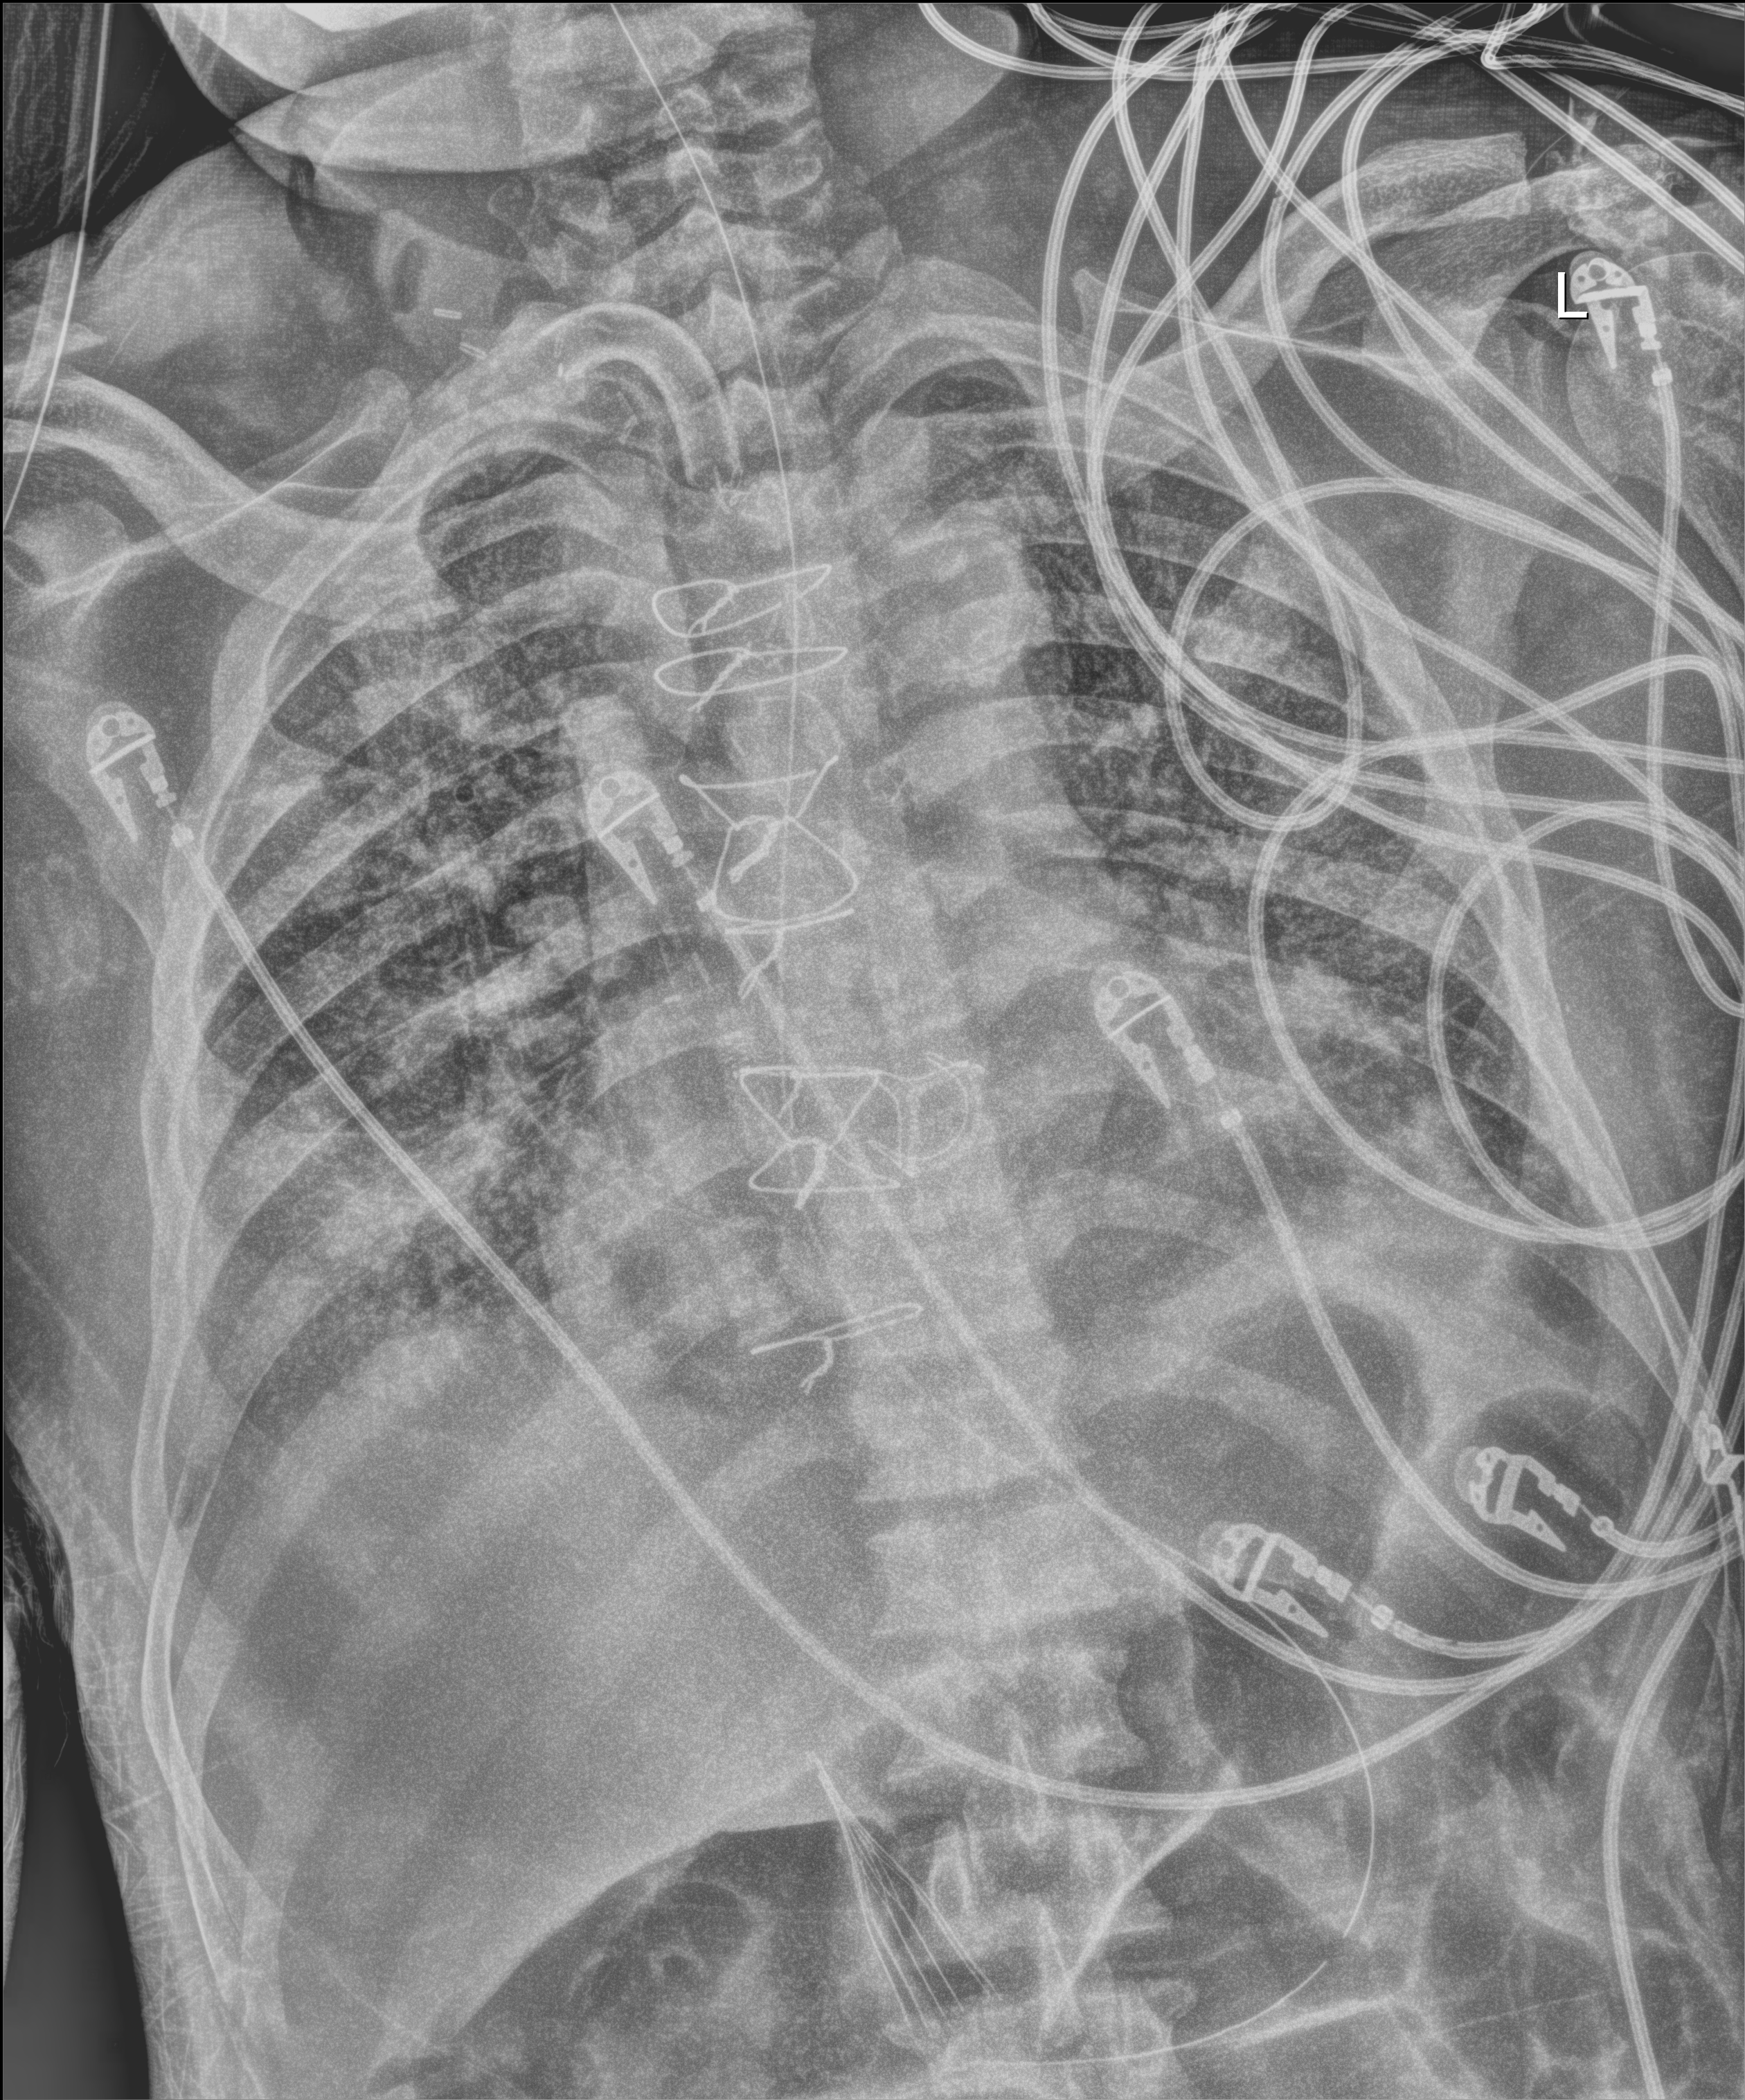
Portable chest radiograph. Patient hospitalised with COVID-19; male, aged 60–74 years.
Hospital-stay facts (about this admission, not read from this image; timing relative to this image not recorded): hypertension (admission record): no; admitted to intensive care during this hospital stay: yes; diabetes (admission record): no.